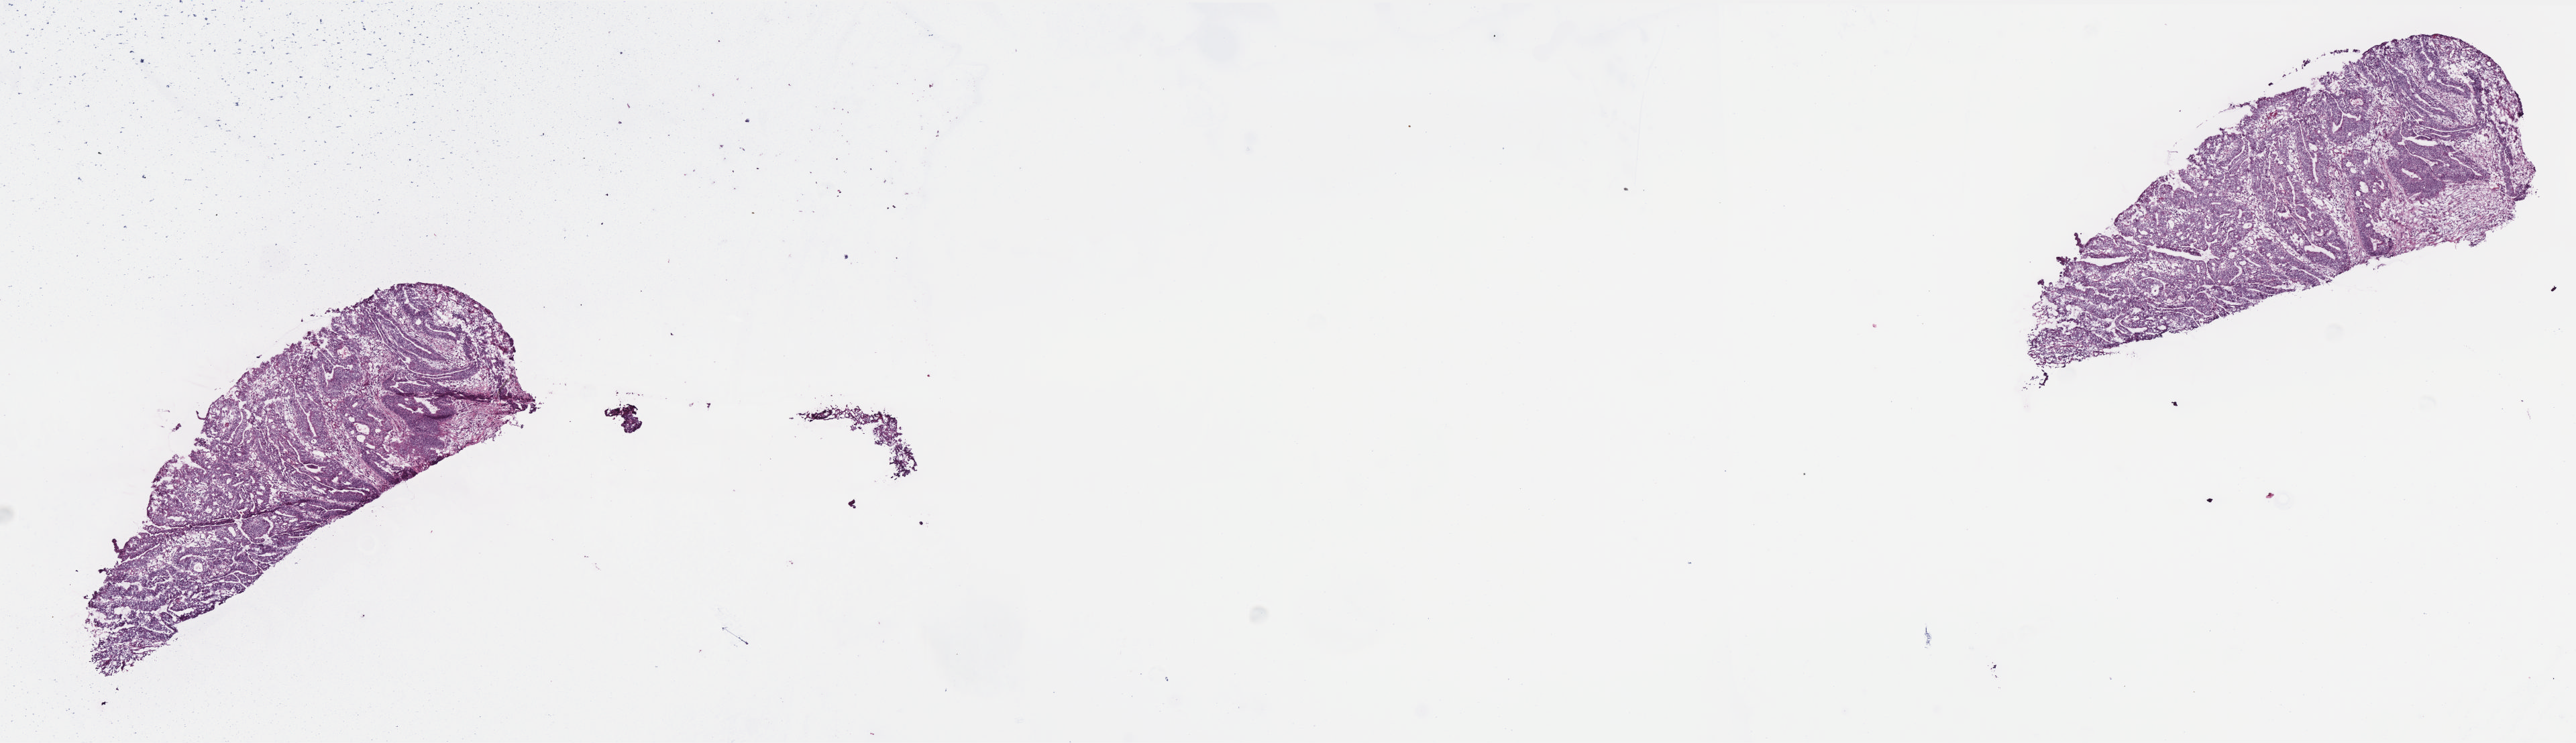
Digitized Hematoxylin and eosin (H&E) stained tissue section (whole slide), a low-resolution overview of the entire scanned area, about 15.4 x 4.4 mm, frozen section from the bottom of the tissue portion, rectum, primary tumour sample. Female, age 59 years at initial diagnosis. Composition of this section per pathologist review: tumour cells 85%, tumour nuclei 85%, normal cells 0%, stromal cells 14%, necrosis 1%. Inflammatory infiltration, as recorded: lymphocyte infiltration 4%, monocyte infiltration 3%, neutrophil infiltration 3%.
• lymph nodes positive (case pathology): 0 of 23 examined
• diagnosis: Adenocarcinoma, NOS
• AJCC pathologic stage: IIA (6th edition)